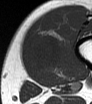
MRI of an extremity soft-tissue mass, one axial slice; position 13 of 62 along the scan axis; MR volume resampled by the dataset authors to the PET/CT grid (not the native acquisition matrix); 3.27 mm slice thickness; 92 × 104 image matrix. Male patient. Case-level facts recorded for this patient, not image findings: histological type: mixoid liposarcoma; grade: low; site of the primary tumour: left thigh.
Structures marked on this image (expert contour drawn on MRI and transferred to this co-registered scan by the dataset authors):
- gross tumour volume (mass): bounding box <28,35,63,73> (left, top, right, bottom; pixels)